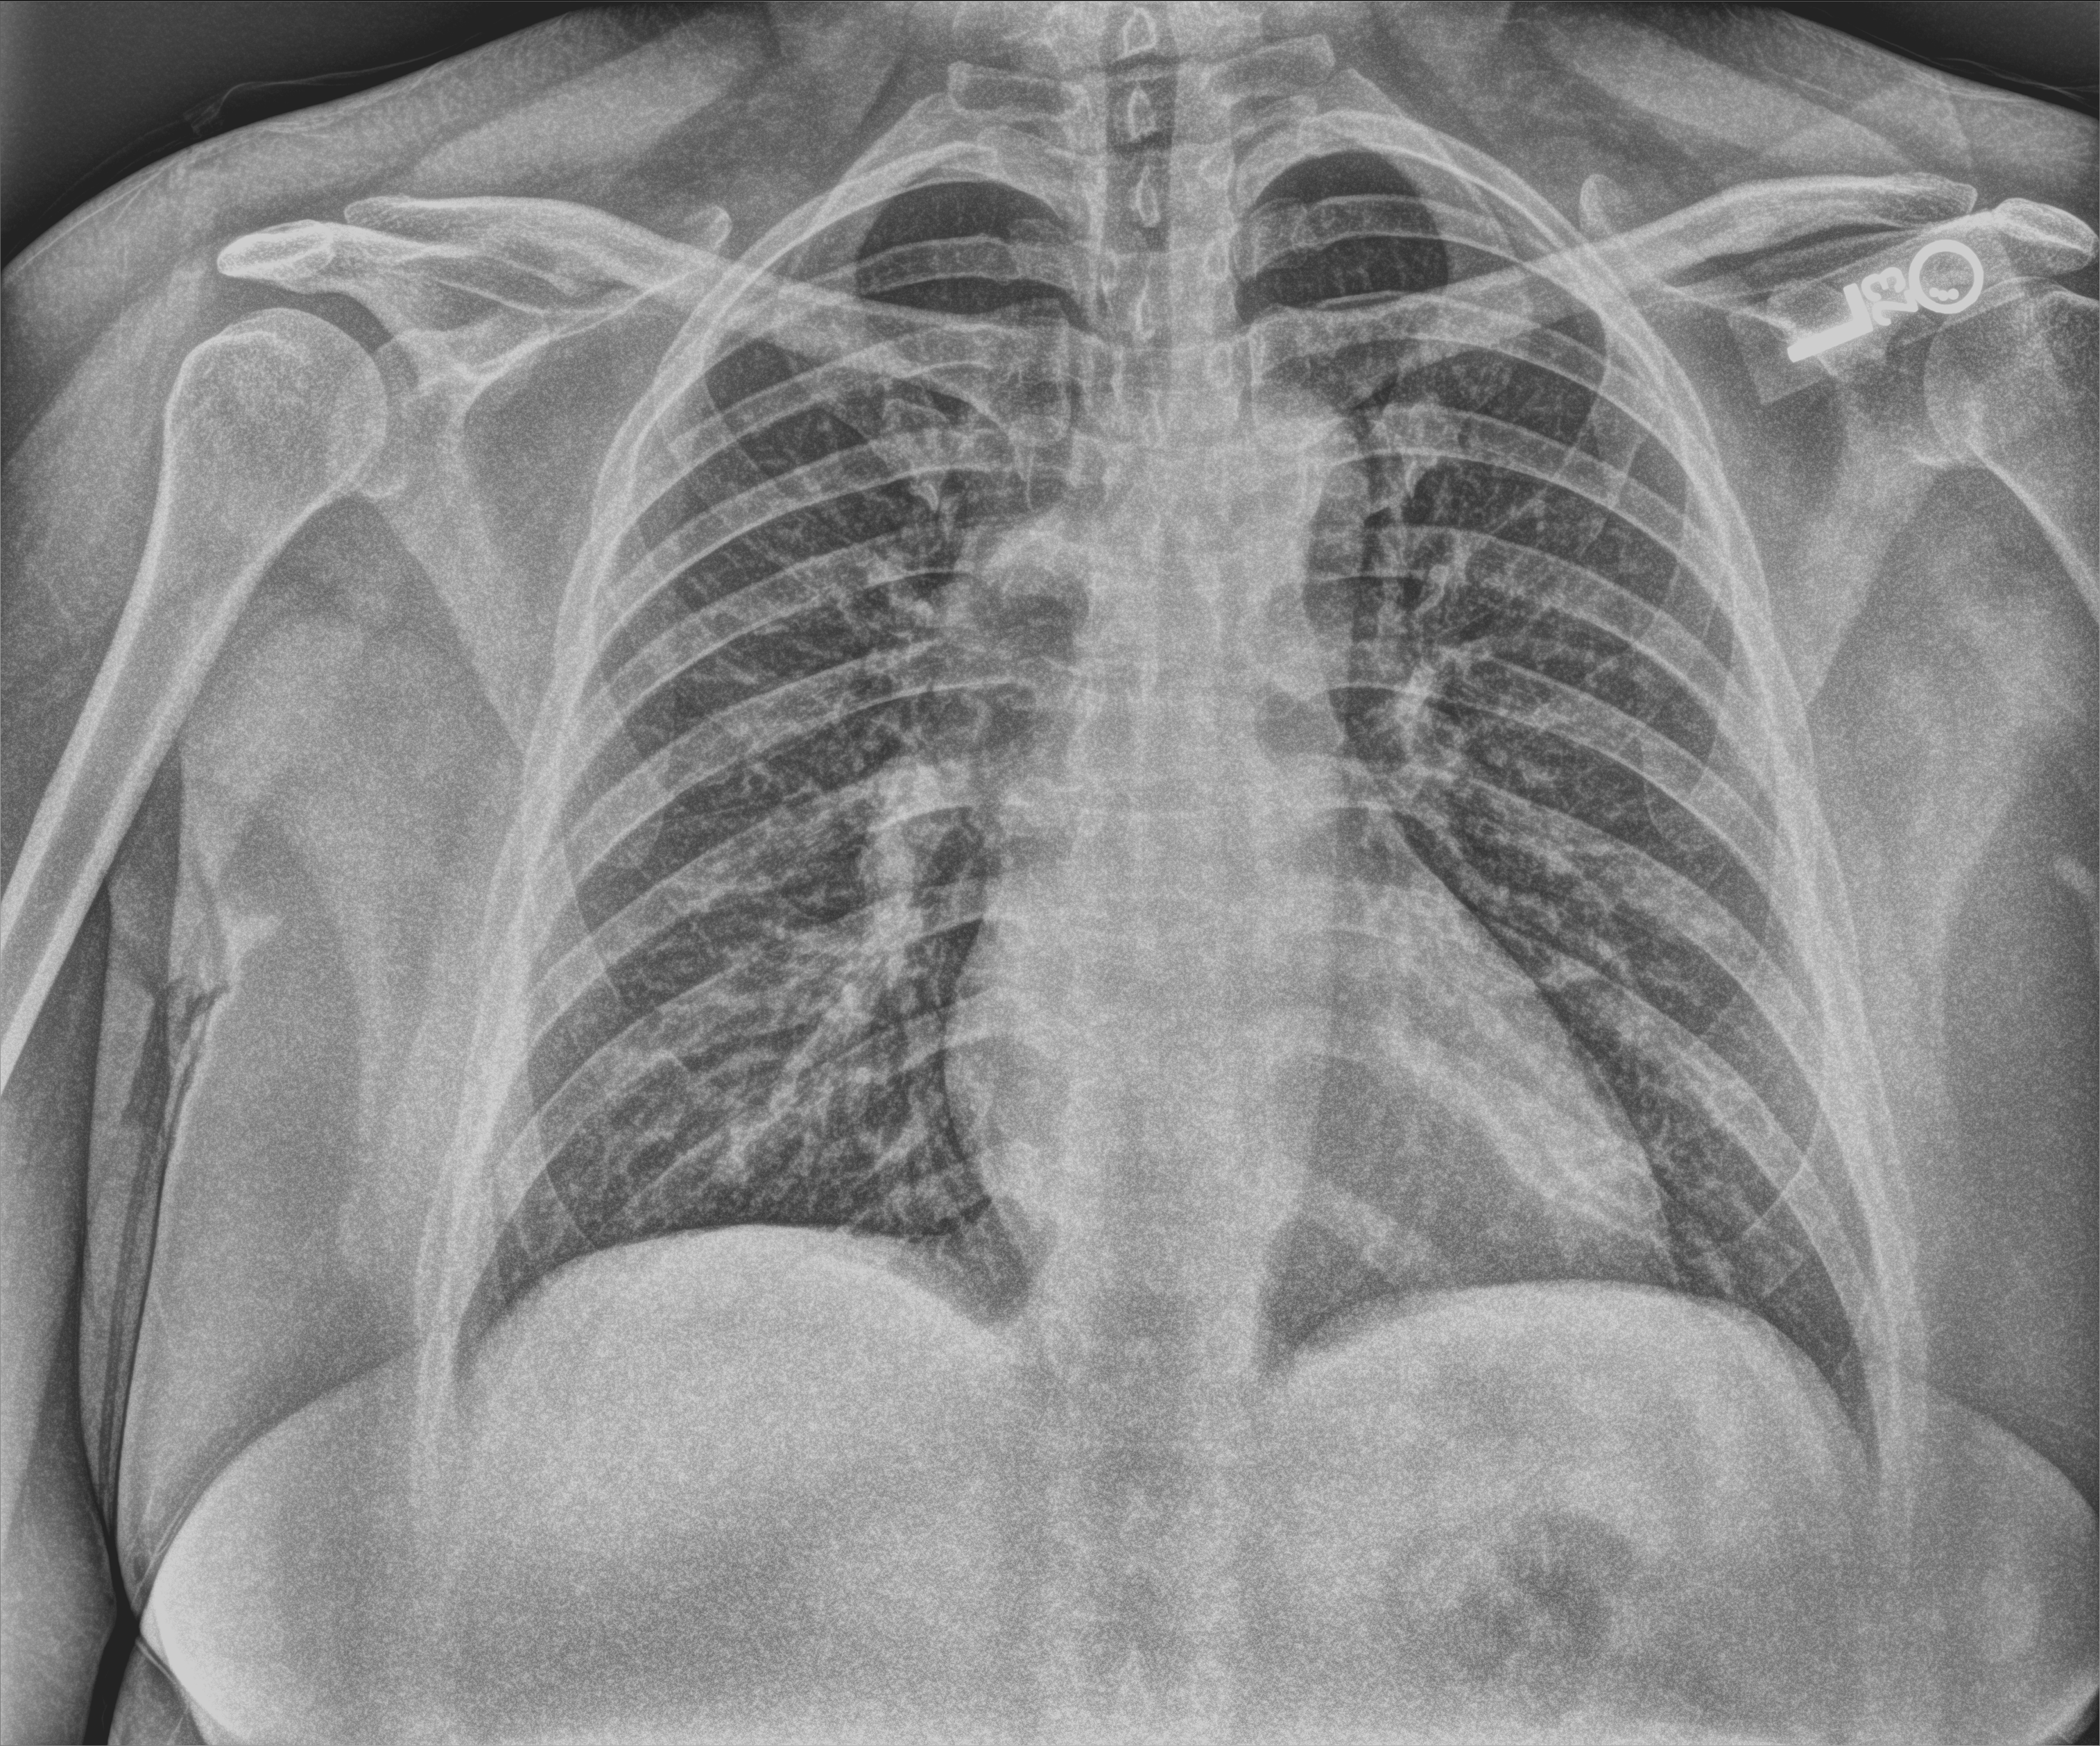
Chest X-ray (portable); anteroposterior (AP) projection. Female patient hospitalised with COVID-19, age 18–59 years.
Admission-level facts for this patient (not findings on this image; timing relative to this image not recorded): length of hospital stay: 1 day; chronic kidney disease (admission record): no; hypertension (admission record): no.